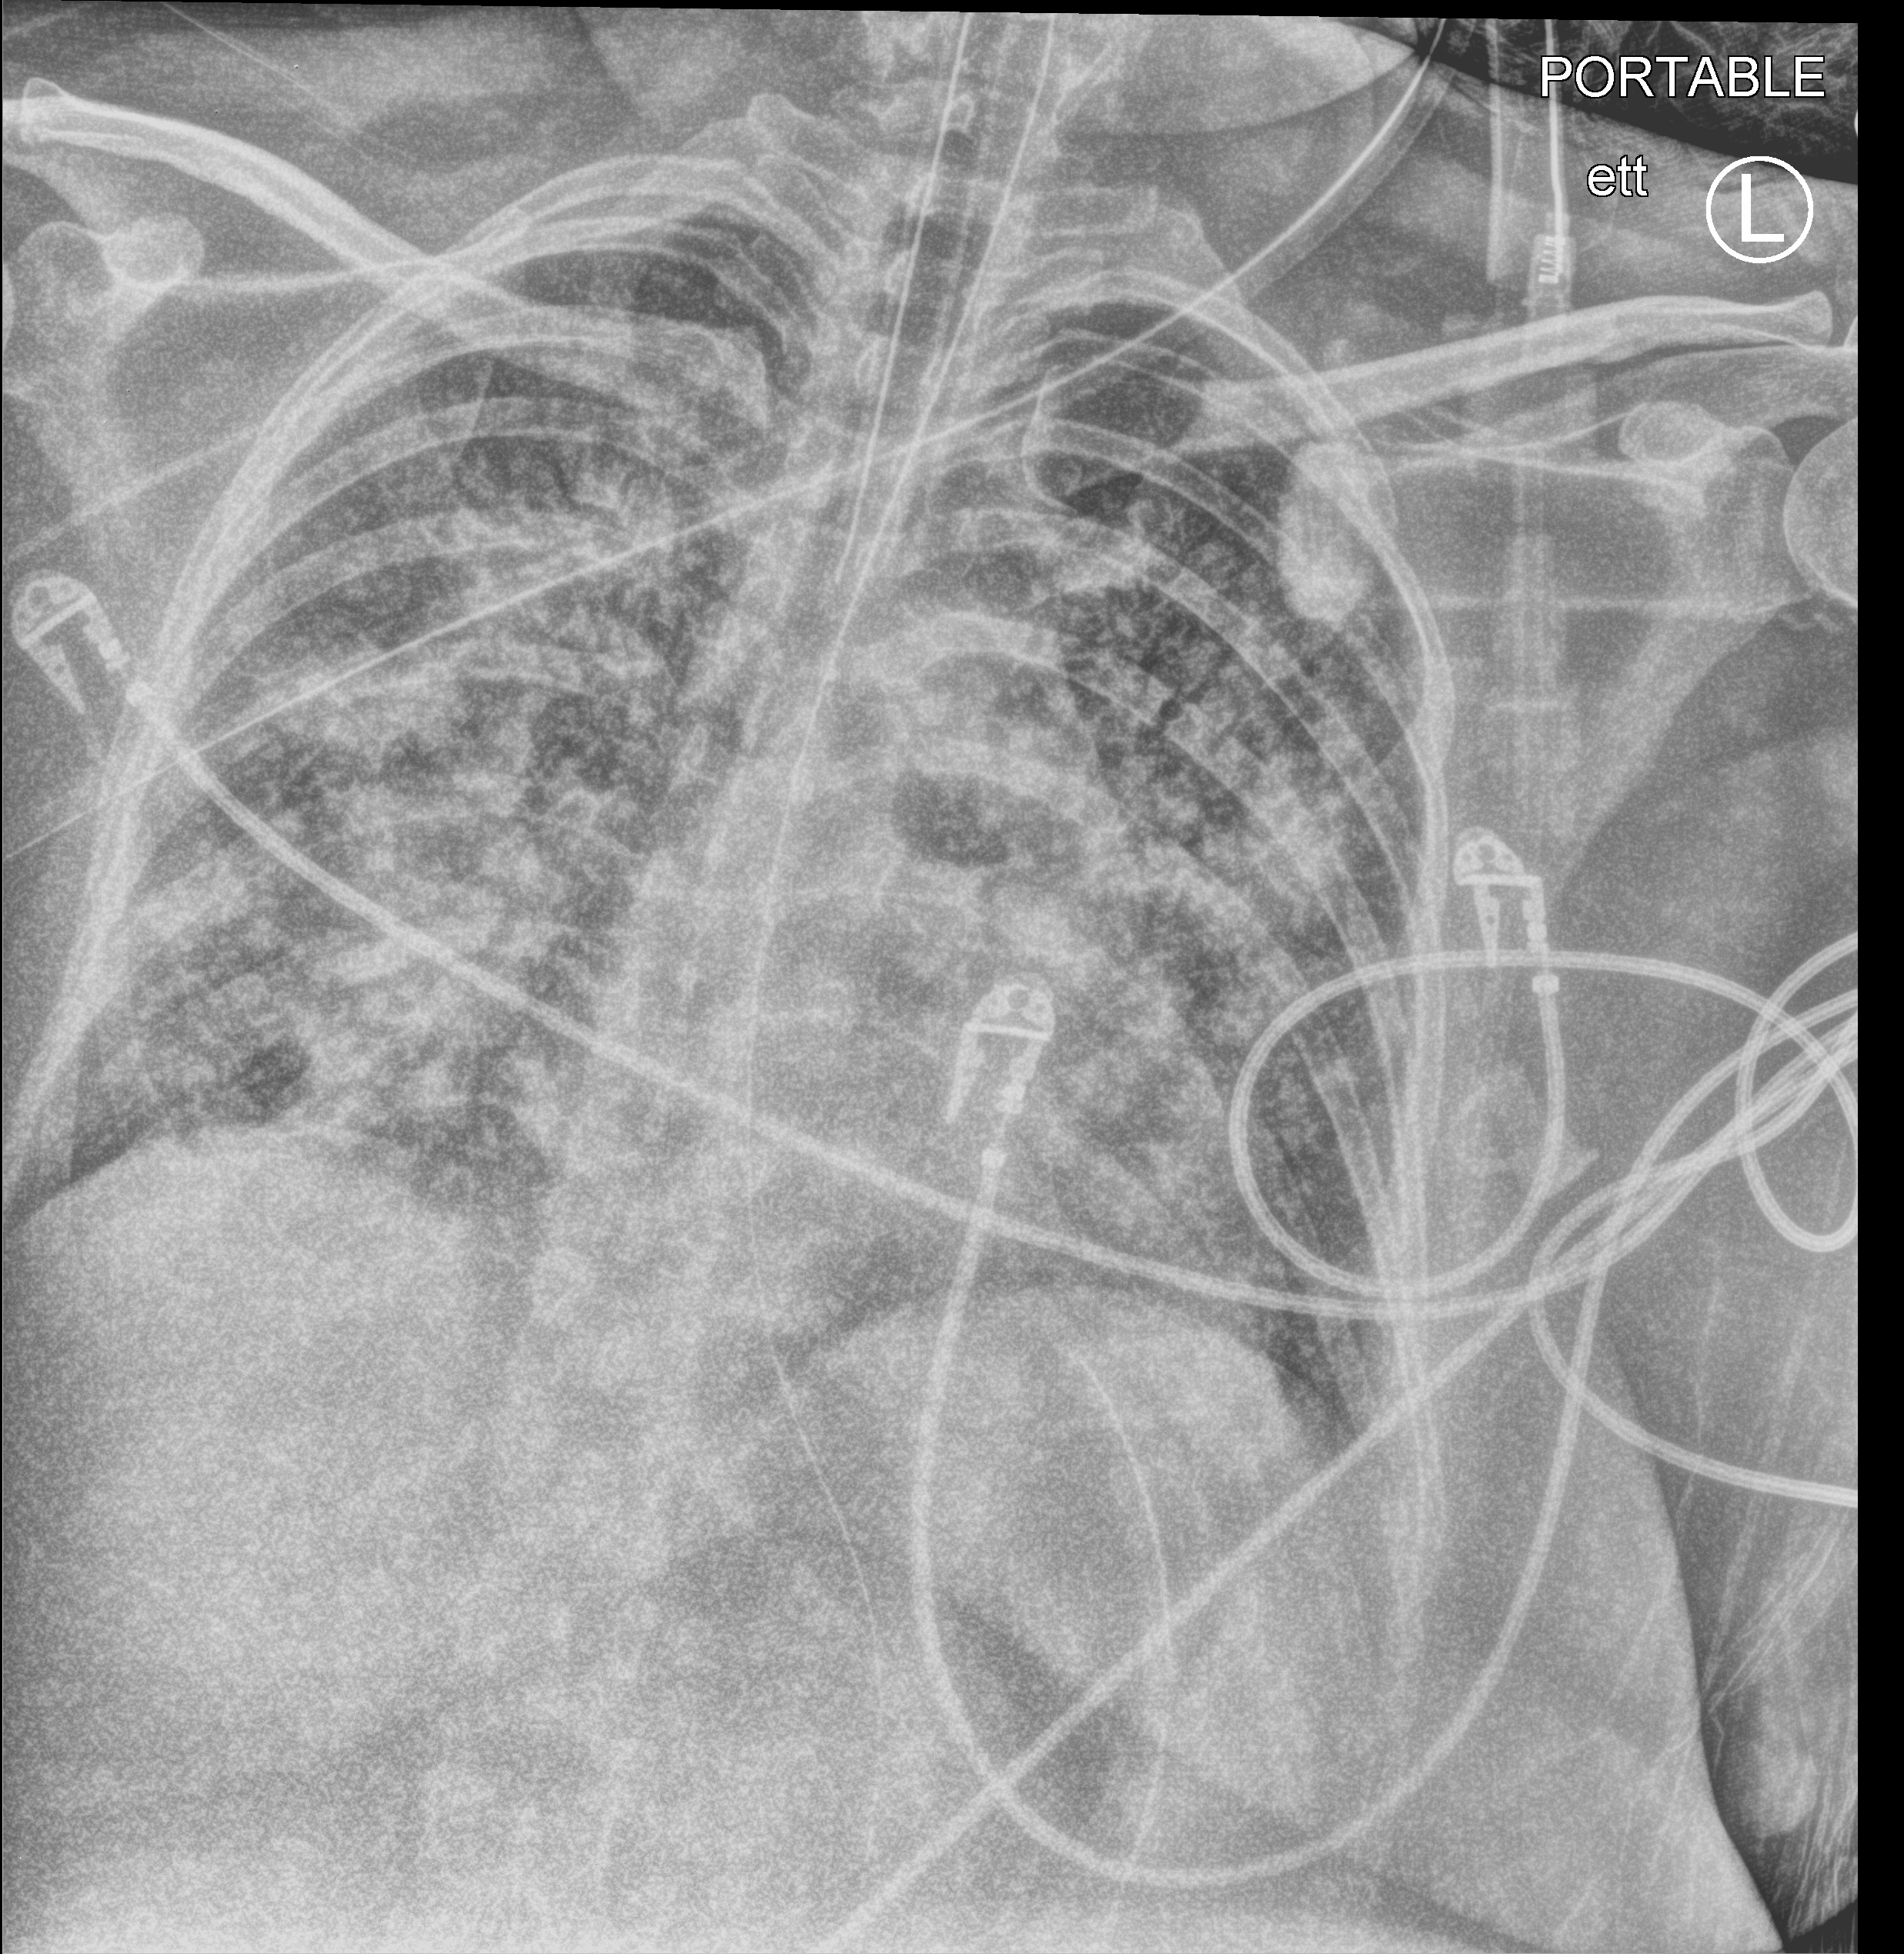
Chest X-ray (portable), anteroposterior (AP) projection. Patient hospitalised with COVID-19, aged 18–59 years.
Admission-level facts for this patient (not findings on this image; timing relative to this image not recorded):
- diabetes (admission record): no